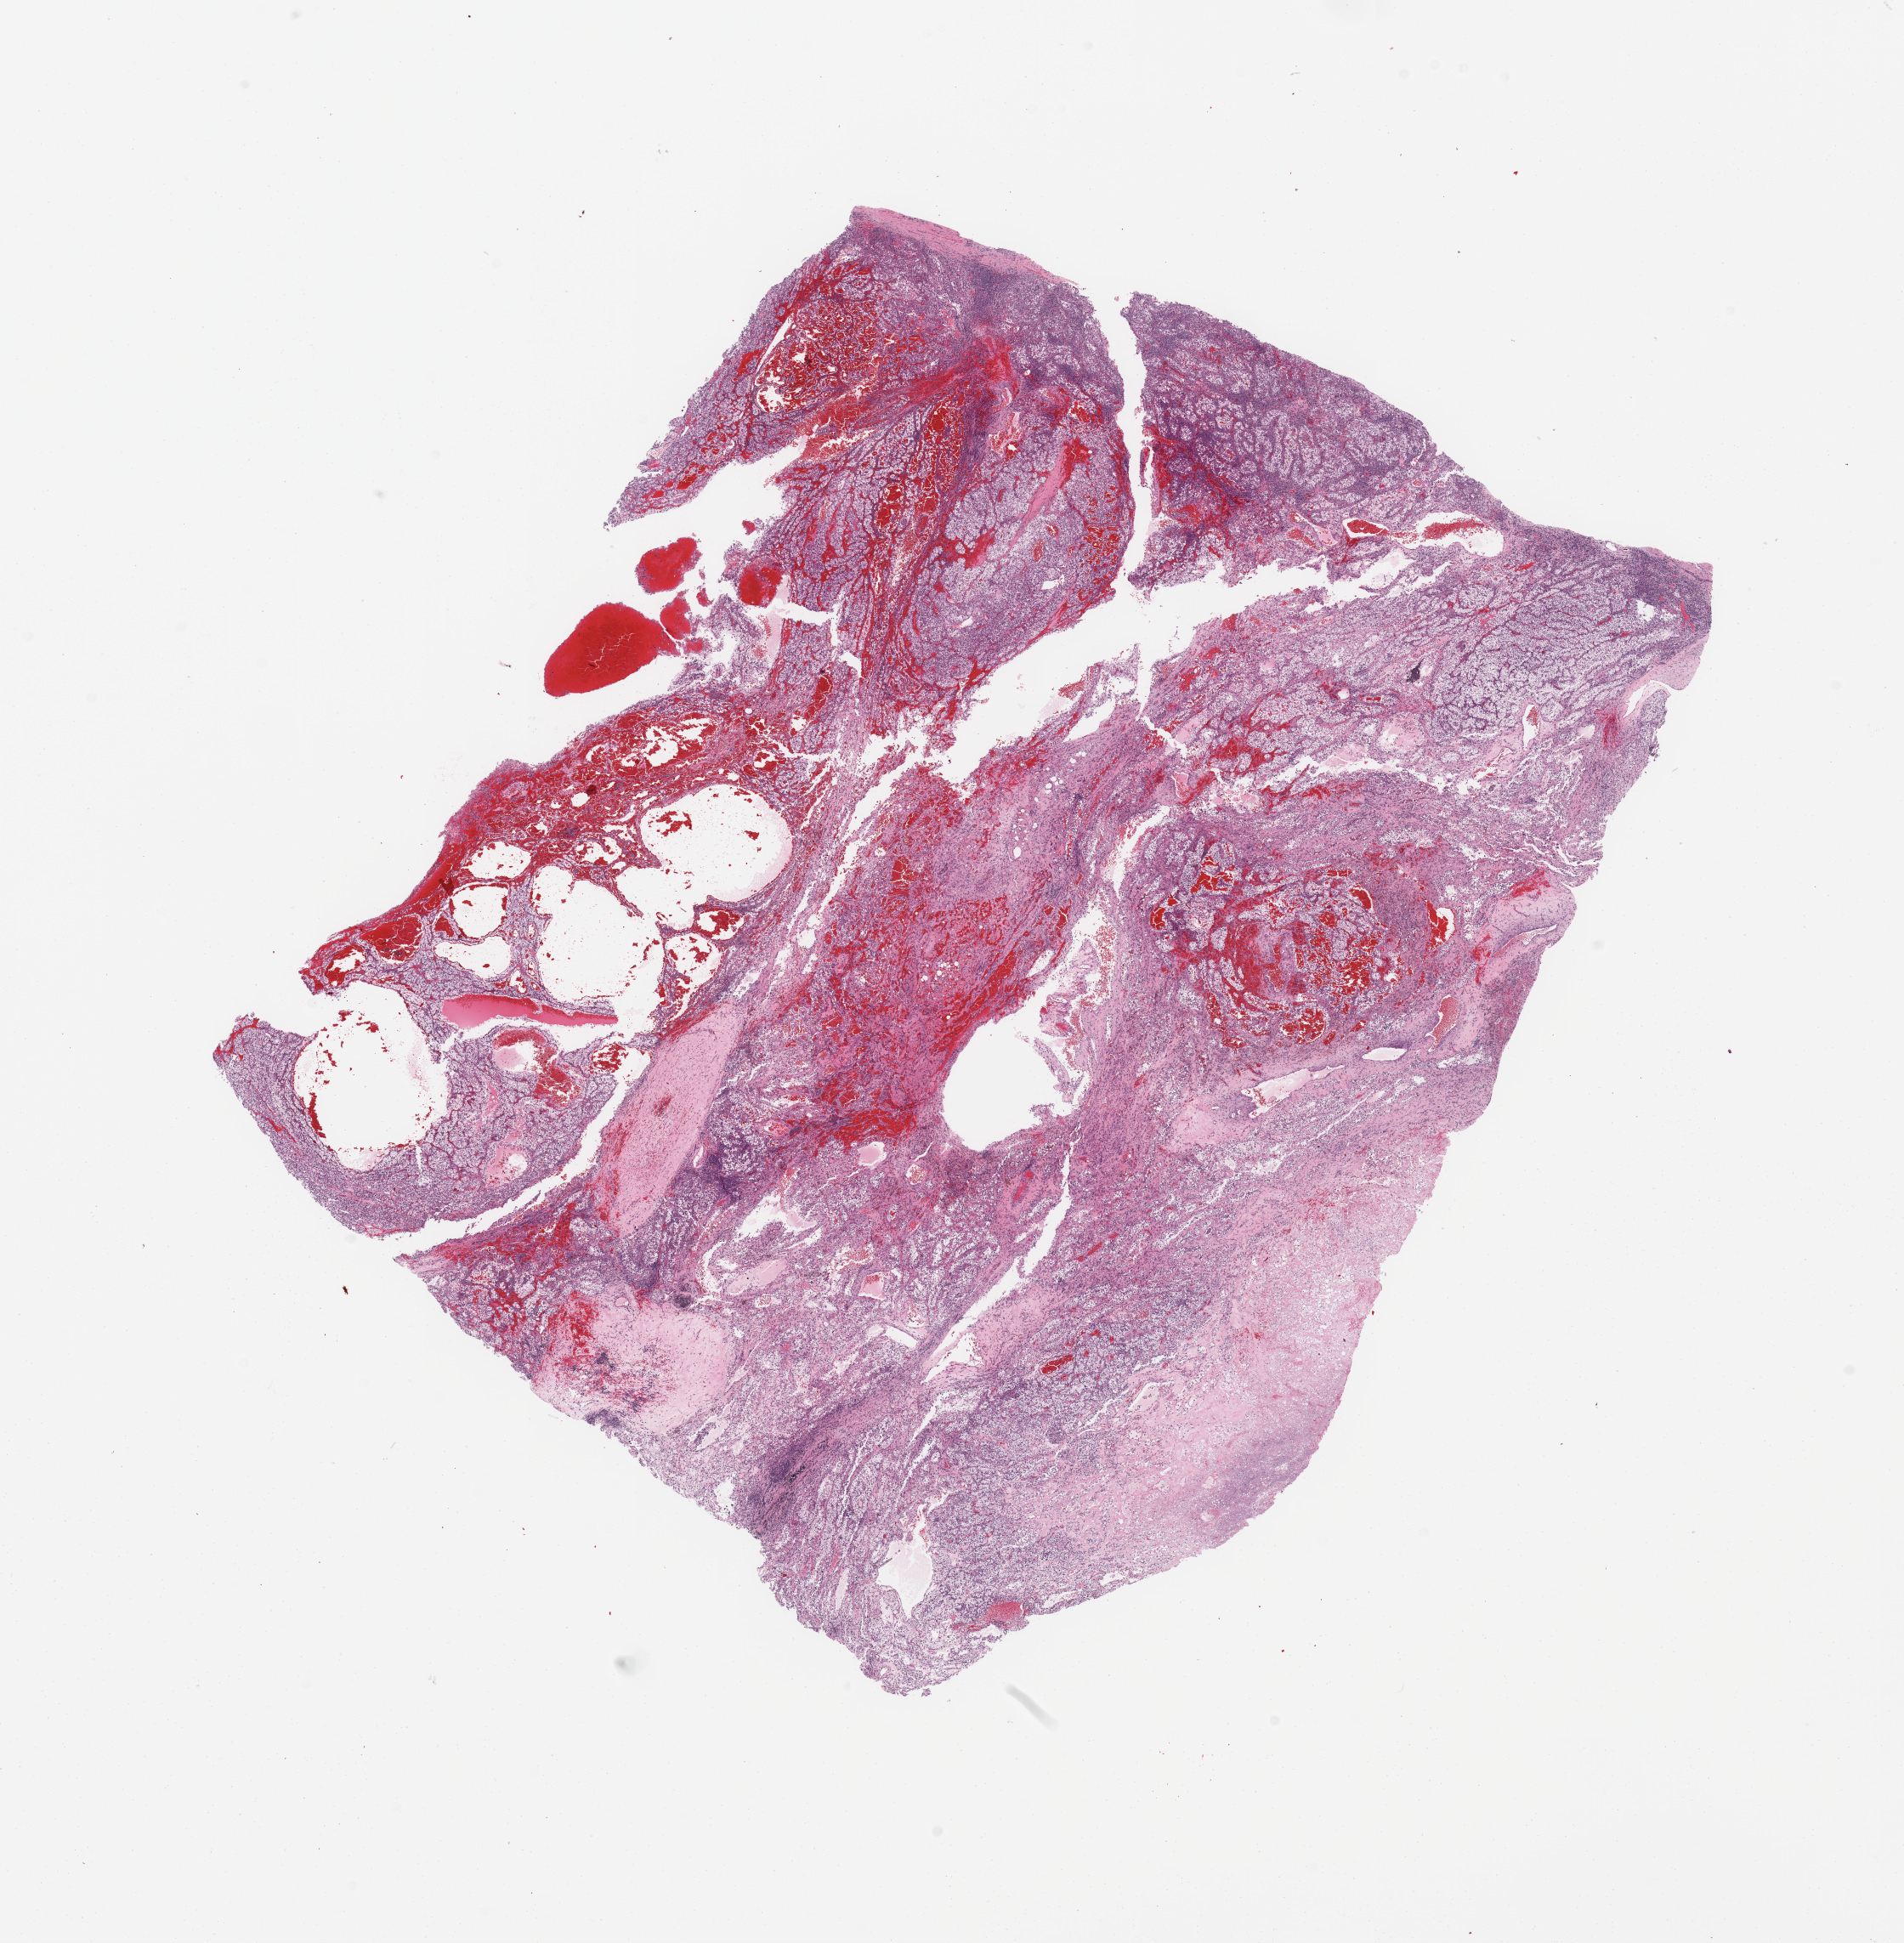
Digitized H&E-stained tissue section (whole slide), shown as a low-resolution overview of the whole scanned area (about 17.7 x 18.1 mm, from a 20x scan), kidney, tumour tissue. 67-year-old female patient. Histologic grade: G3 (poorly differentiated).
- diagnosis: Renal cell carcinoma, NOS
- primary tumour site (as recorded): lower pole
- AJCC pathologic stage: I